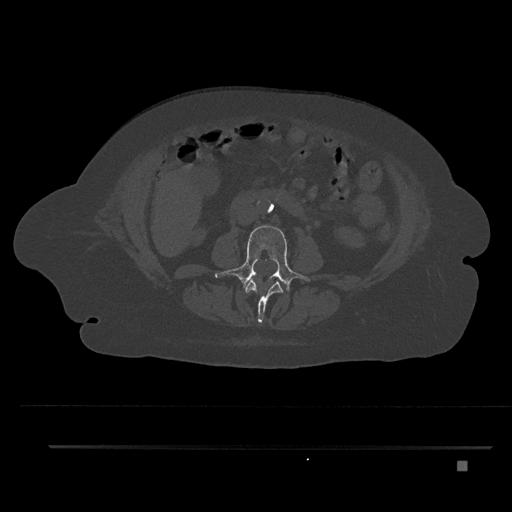
CT including the spine, one axial slice. Slice 139 of 797 in the series (ordered by position). Reconstruction kernel Br40s/3. 120 kVp. Bone window (W 1800 / L 400 HU). 0.5 mm slice thickness. 512 × 512 image matrix, field of view 437 × 437 mm. Patient: female, 76 years. From the clinical record (not read from this slice): primary cancer: lung; vertebrae with lytic lesions (as recorded): T11, L3.
Outlined on this slice (semi-automatically segmented with operator editing):
- L2 vertebra: box from (x=245, y=278) to (x=283, y=323) px
- L3 vertebra: (x=215, y=225)–(x=309, y=292)